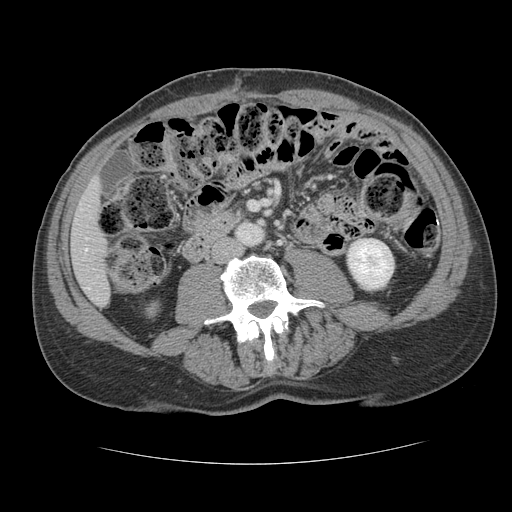
Contrast-enhanced abdominal CT, one axial slice. Slice 30 of 134 in the series (ordered by position). Intravenous contrast given. Soft-tissue window (W 400 / L 40 HU). 2.5 mm slice thickness. 512 × 512 image matrix, field of view 377 × 377 mm. Male patient, age 68 years. Case-level facts recorded for this patient, not image findings: diagnosis: colorectal cancer liver metastases, imaged before liver resection; multiple liver metastases: yes; largest metastasis: 2.2 cm; disease in both lobes: no.
Annotated regions visible in this slice (manually delineated by an expert):
- hepatic veins: bounding box [x1, y1, x2, y2] px = [85, 248, 87, 250]
- liver: [72, 183, 110, 305]
- planned liver remnant (the part of the liver to remain after resection): [72, 183, 110, 306]